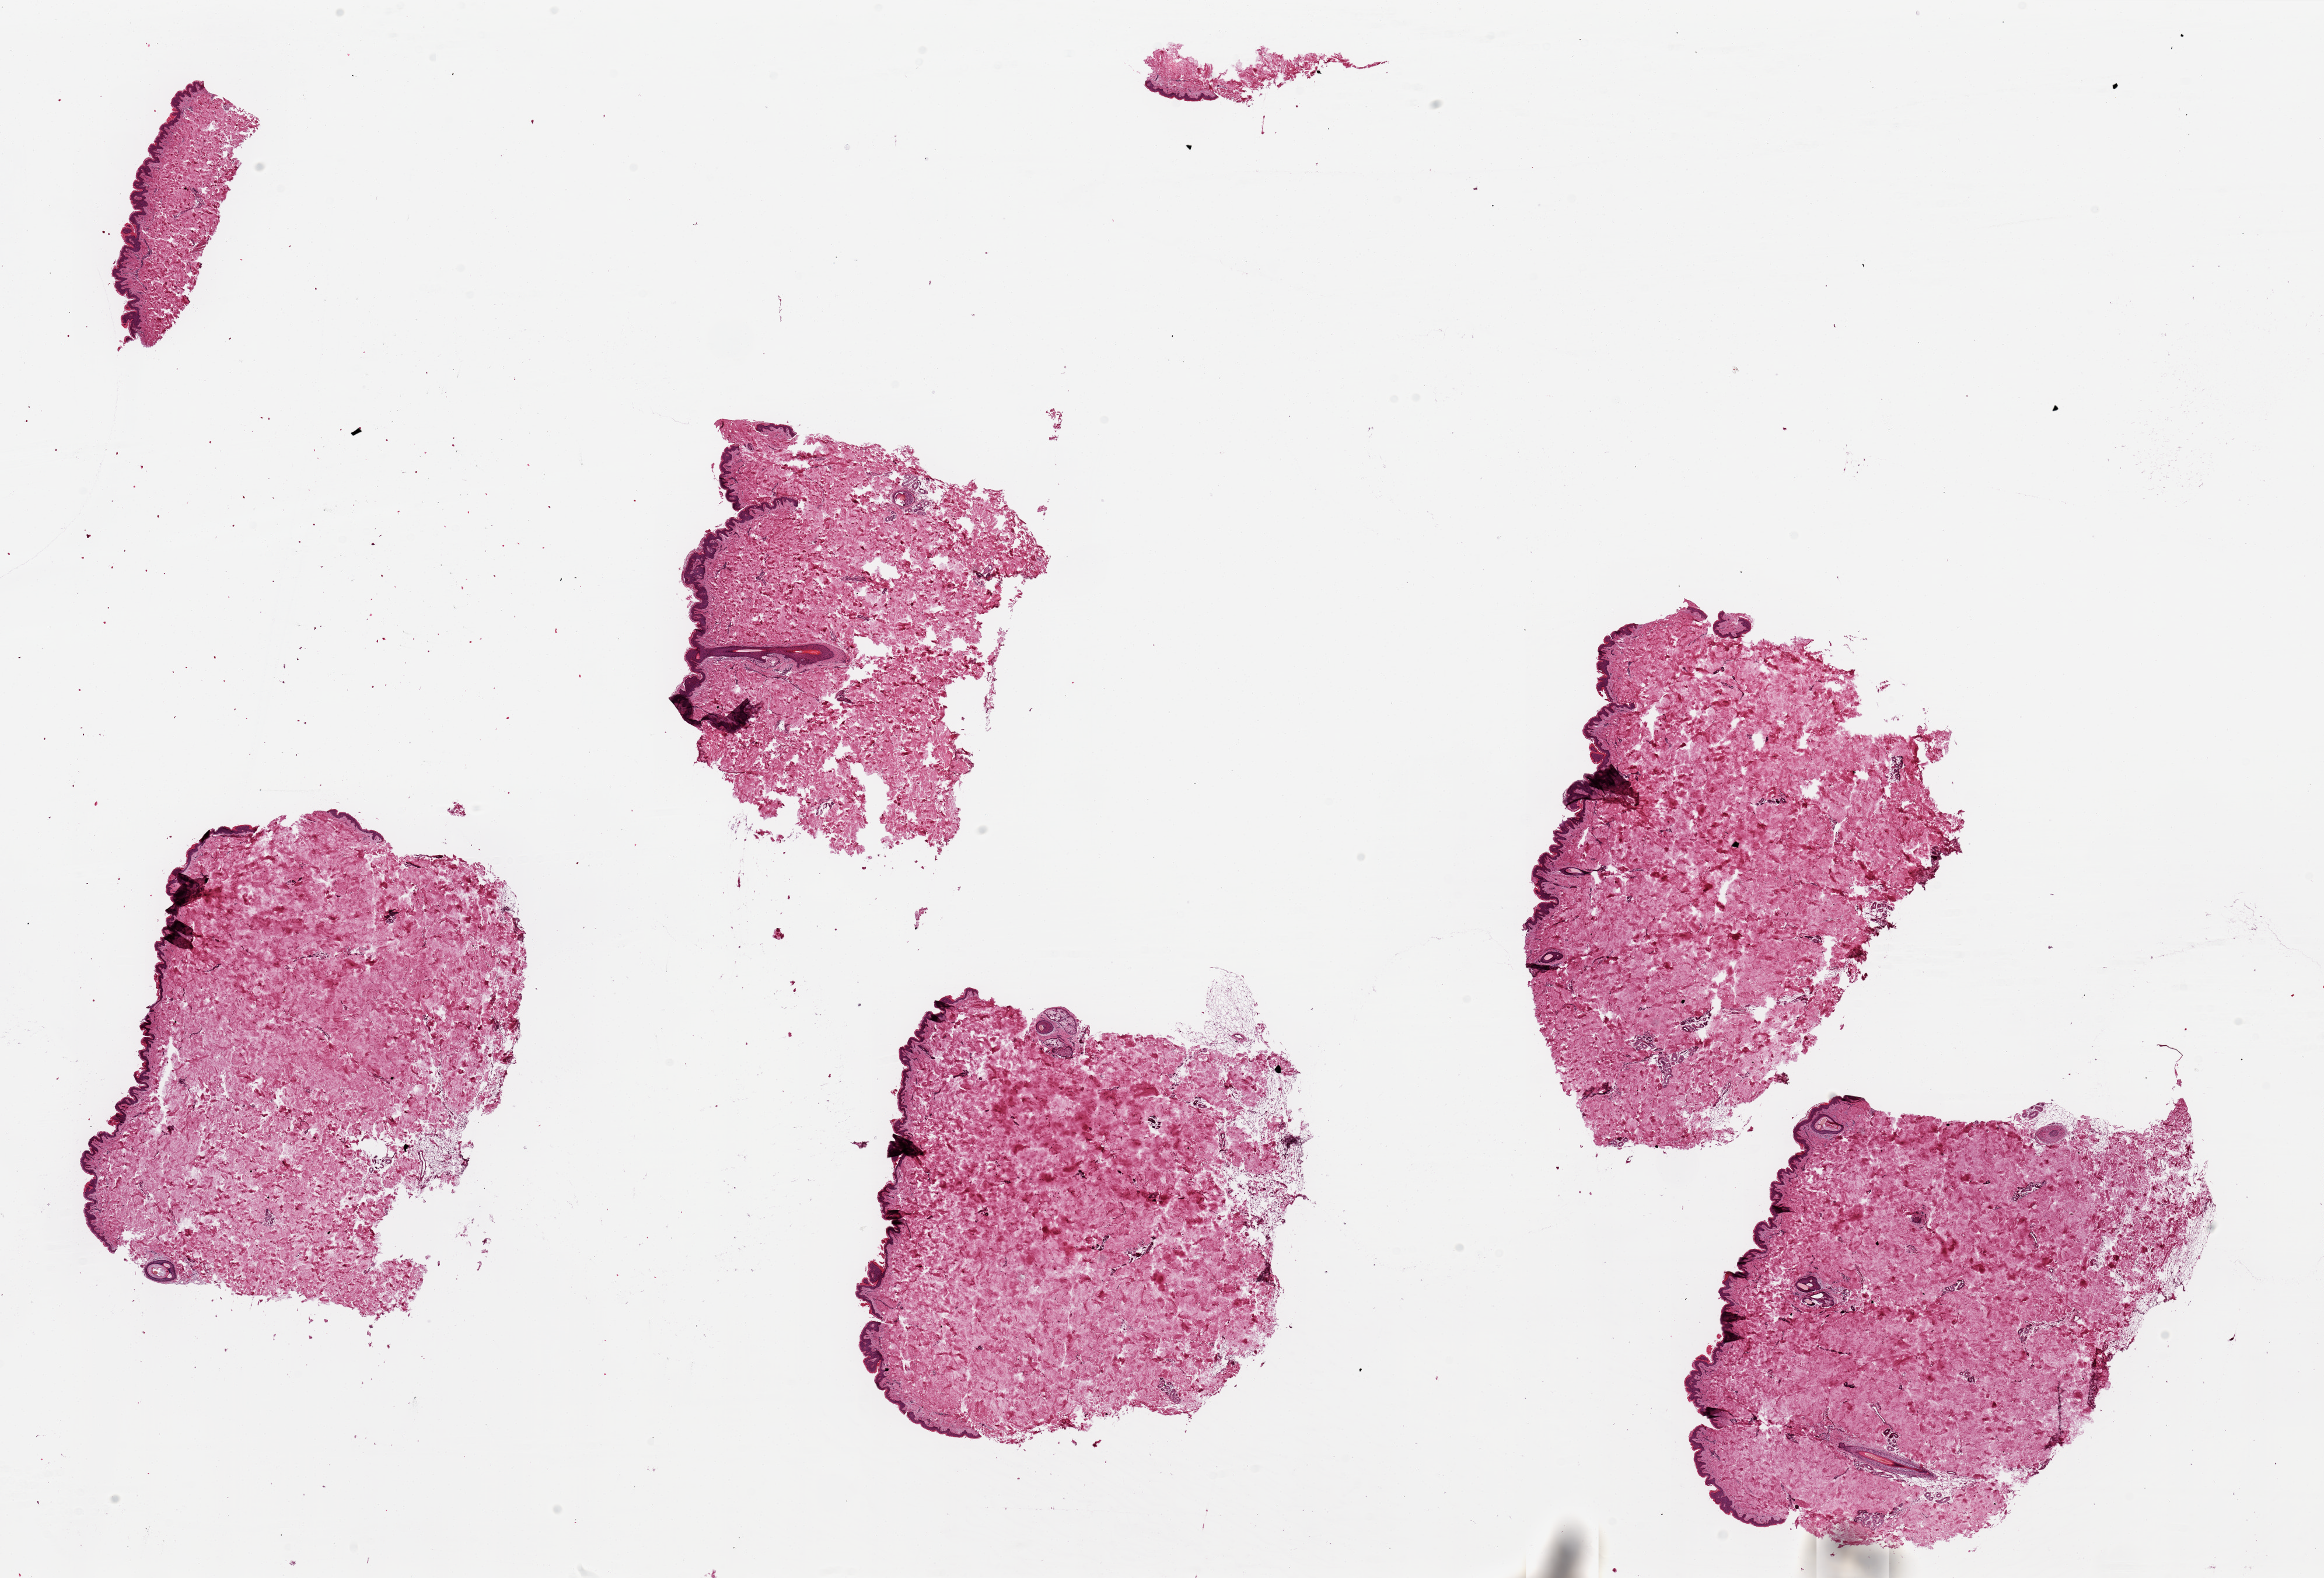
Whole-slide image, H&E stain, whole scanned area (about 31.5 x 21.4 mm, acquisition: 20x scan) shown as a low-resolution overview. PAXgene-fixed, paraffin-embedded tissue. Target tissue: skin of suprapubic region. Tissue donor sample. Male donor.
Reviewer comment on this tissue sample: 6 pieces ~6x5mm, squamous epithelium is ~1% thickness.